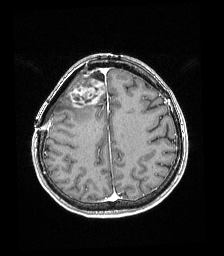
Brain MRI from a brain-tumour surgery series, one axial slice; slice 63 of 192 in the series (ordered by position); T1-weighted post-contrast; 224 × 256 image matrix, field of view 219 × 250 mm. Case-level facts recorded for this patient, not image findings: histopathology: Astrocytoma; WHO grade: 4; IDH mutation: yes.
Outlined on this slice (outlined manually by an expert reader):
- tumour: bounding box (x1, y1, x2, y2) in pixels: (69, 80, 104, 108)